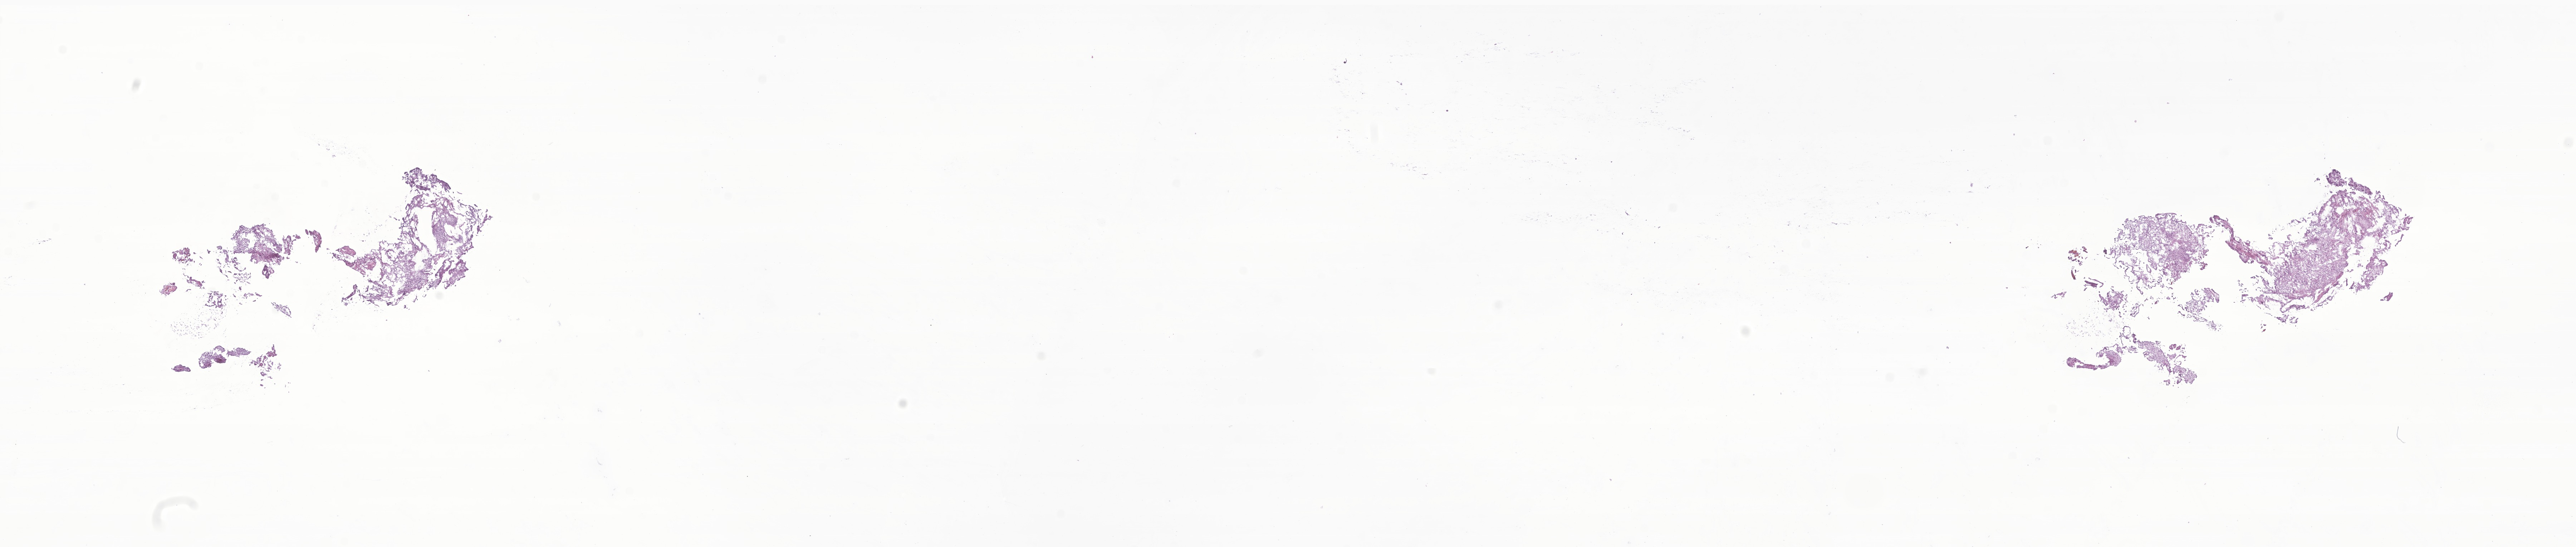
Whole-slide image, haematoxylin and eosin stain of tumor tissue from the brain — a low-resolution overview of the entire scanned area, about 30.4 x 6.4 mm. Frozen section (OCT-embedded). Male patient, age 191 months (15 years 11 months).
- recorded diagnosis: Neoplasm, malignant